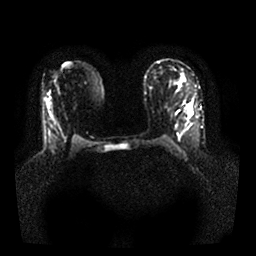
Breast MRI, one axial slice; slice 14 of 25 in the series (ordered by position); diffusion-weighted series; image 2 of 4 stored at this slice position (different b-values; order by instance number); 1.5 T; 4 mm slice thickness; 256 × 256 image matrix. Female patient.
Annotated regions visible in this slice (manually delineated by an expert):
- tumour on diffusion-weighted imaging: box from (x=188, y=105) to (x=192, y=110) px